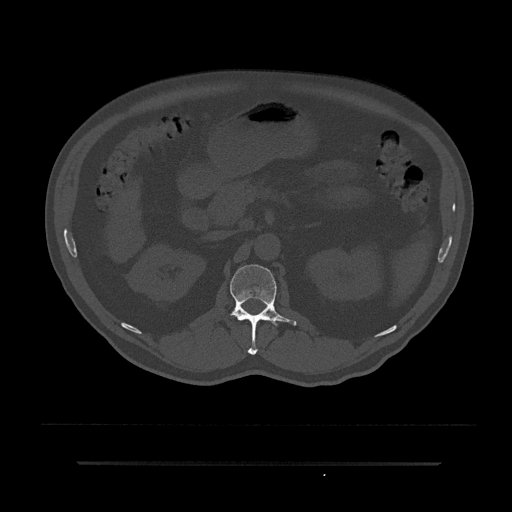
CT including the spine, one axial slice. Position 144 of 797 along the scan axis. Bone window (W 1800 / L 400 HU). 0.5 mm slice thickness. 512 × 512 image matrix, field of view 464 × 464 mm. Male patient, age 59 years. From the clinical record (not read from this slice): primary cancer: bile ducts.
Structures marked on this image (semi-automatically segmented with operator editing):
- L1 vertebra: bounding box [x1, y1, x2, y2] px = [230, 265, 297, 355]